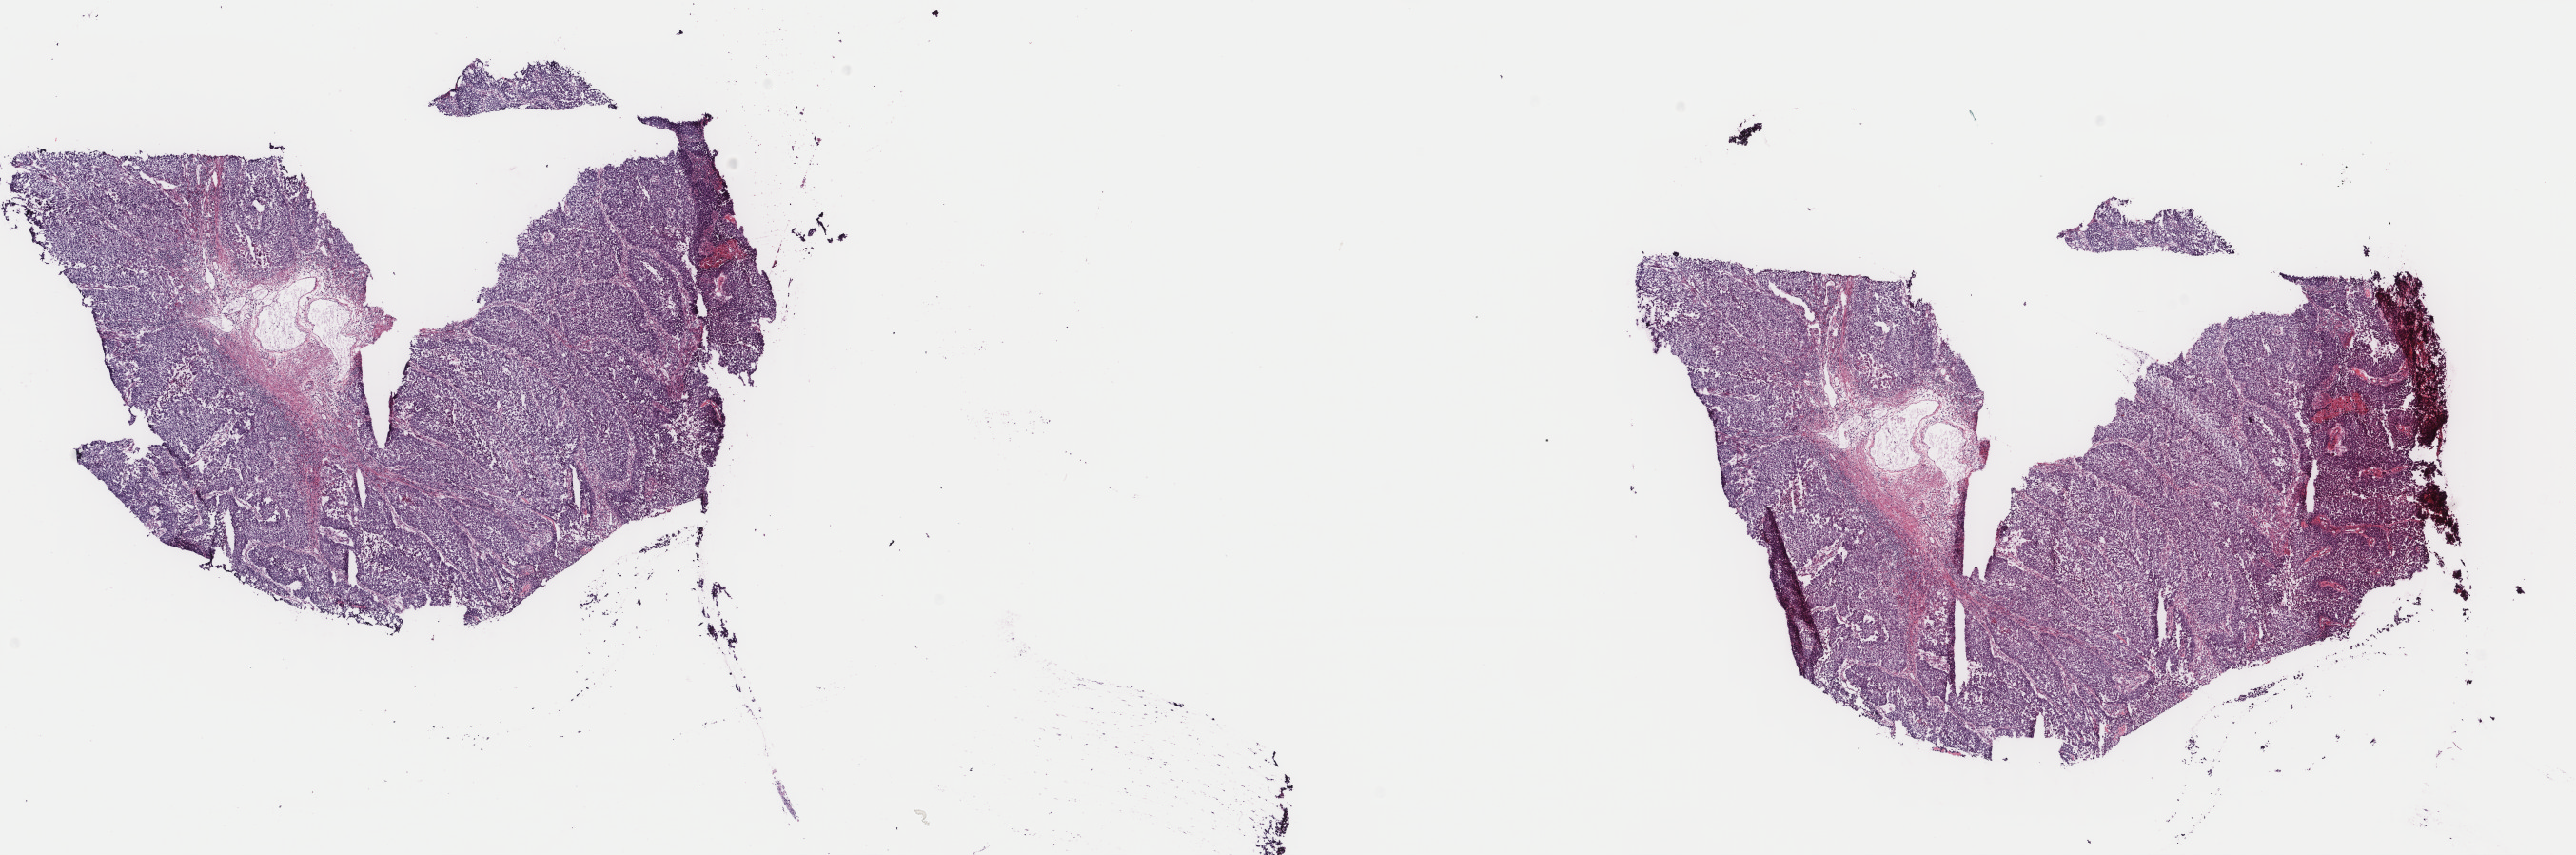
Digitized H&E-stained tissue section (whole slide) — a low-resolution overview of the entire scanned area, about 21.5 x 7.1 mm; frozen section from the top of the tissue portion; primary tumour sample from the bladder. Male, age 54 years at initial diagnosis. Histologic grade: high grade. Composition of this section per pathologist review: tumour cells 85%, tumour nuclei 95%, normal cells 0%, stromal cells 10%, necrosis 5%. Inflammatory infiltration, as recorded: lymphocyte infiltration 0%, monocyte infiltration 0%, neutrophil infiltration 0%.
* AJCC pathologic stage: II
* pathologic diagnosis: Papillary transitional cell carcinoma